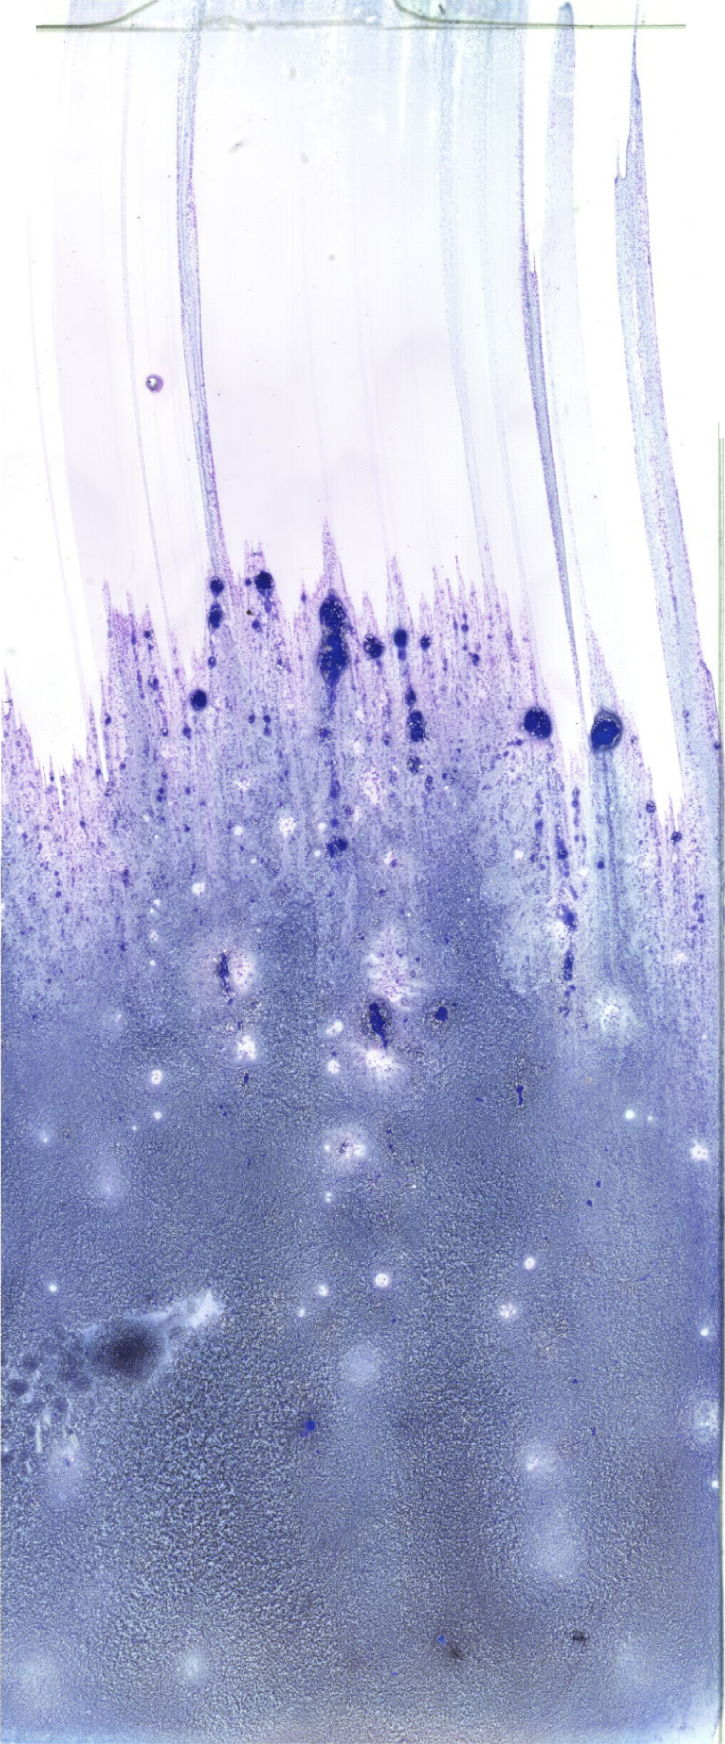
Whole-slide image of a May-Grünwald-Giemsa (MGG)-stained bone marrow aspirate smear — low-resolution overview of the scanned area, about 20.6 x 49.4 mm. Patient sex: male.
Diagnosis: Acute Myeloid Leukemia without Maturation.